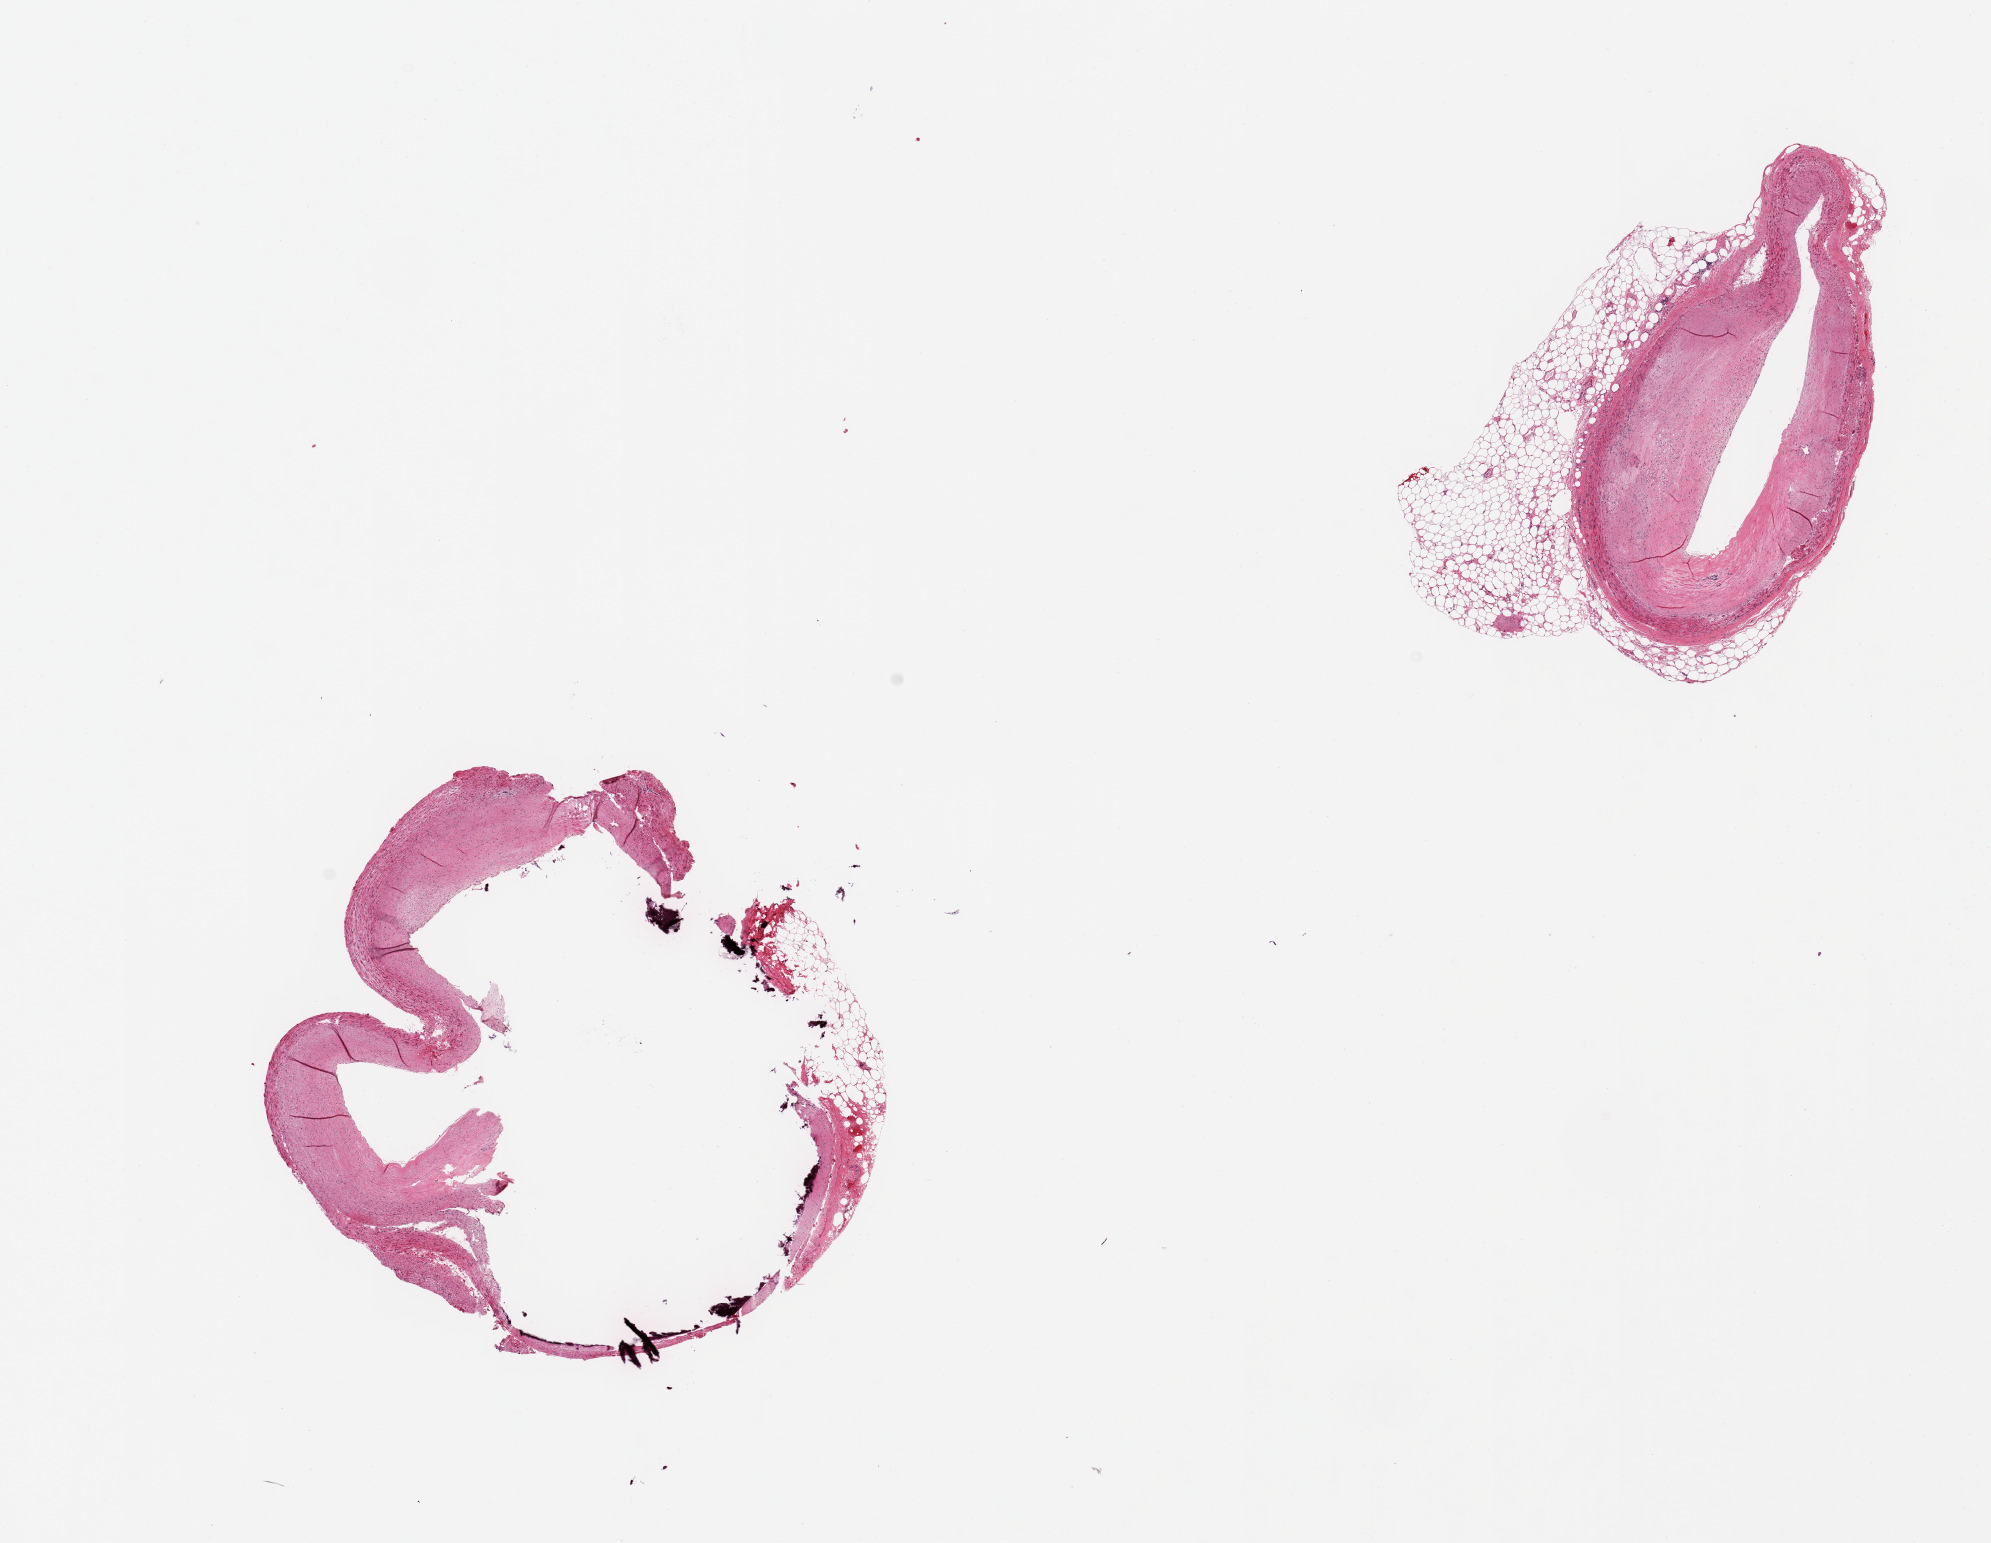
Digitized hematoxylin and eosin (H&E)-stained section — whole scanned area (about 15.8 x 12.2 mm) shown as a low-resolution overview. PAXgene-fixed, paraffin-embedded tissue. Sampled site (target tissue): coronary artery. Donor tissue sample. Donor sex: male.
* pathologist's review note for this sample: 2 pieces 80% occlusive focally calcified atherosis